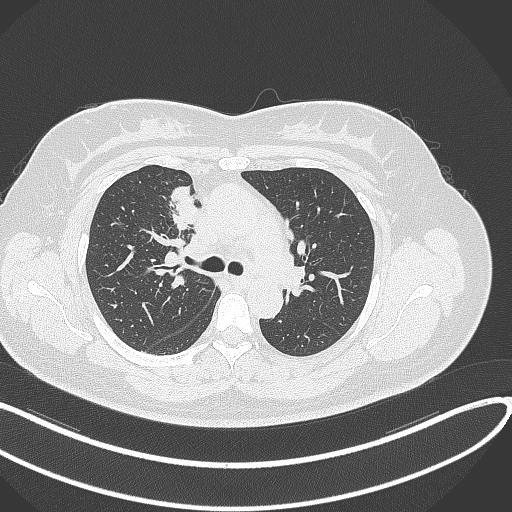
Chest CT, one axial slice. Slice 184 of 303 in the series (ordered by position). 120 kVp. Lung window (W 1500 / L -600 HU). 1 mm slice thickness. 512 × 512 image matrix, field of view 400 × 400 mm. Female patient, age 46 years. Case-level facts recorded for this patient, not image findings: clinical TNM (as recorded): T2a N1 M0.
Outlined on this slice (rectangle marked by the reading radiologist):
- lung tumour (recorded histology: adenocarcinoma): bounding box <169,183,200,232> (left, top, right, bottom; pixels)